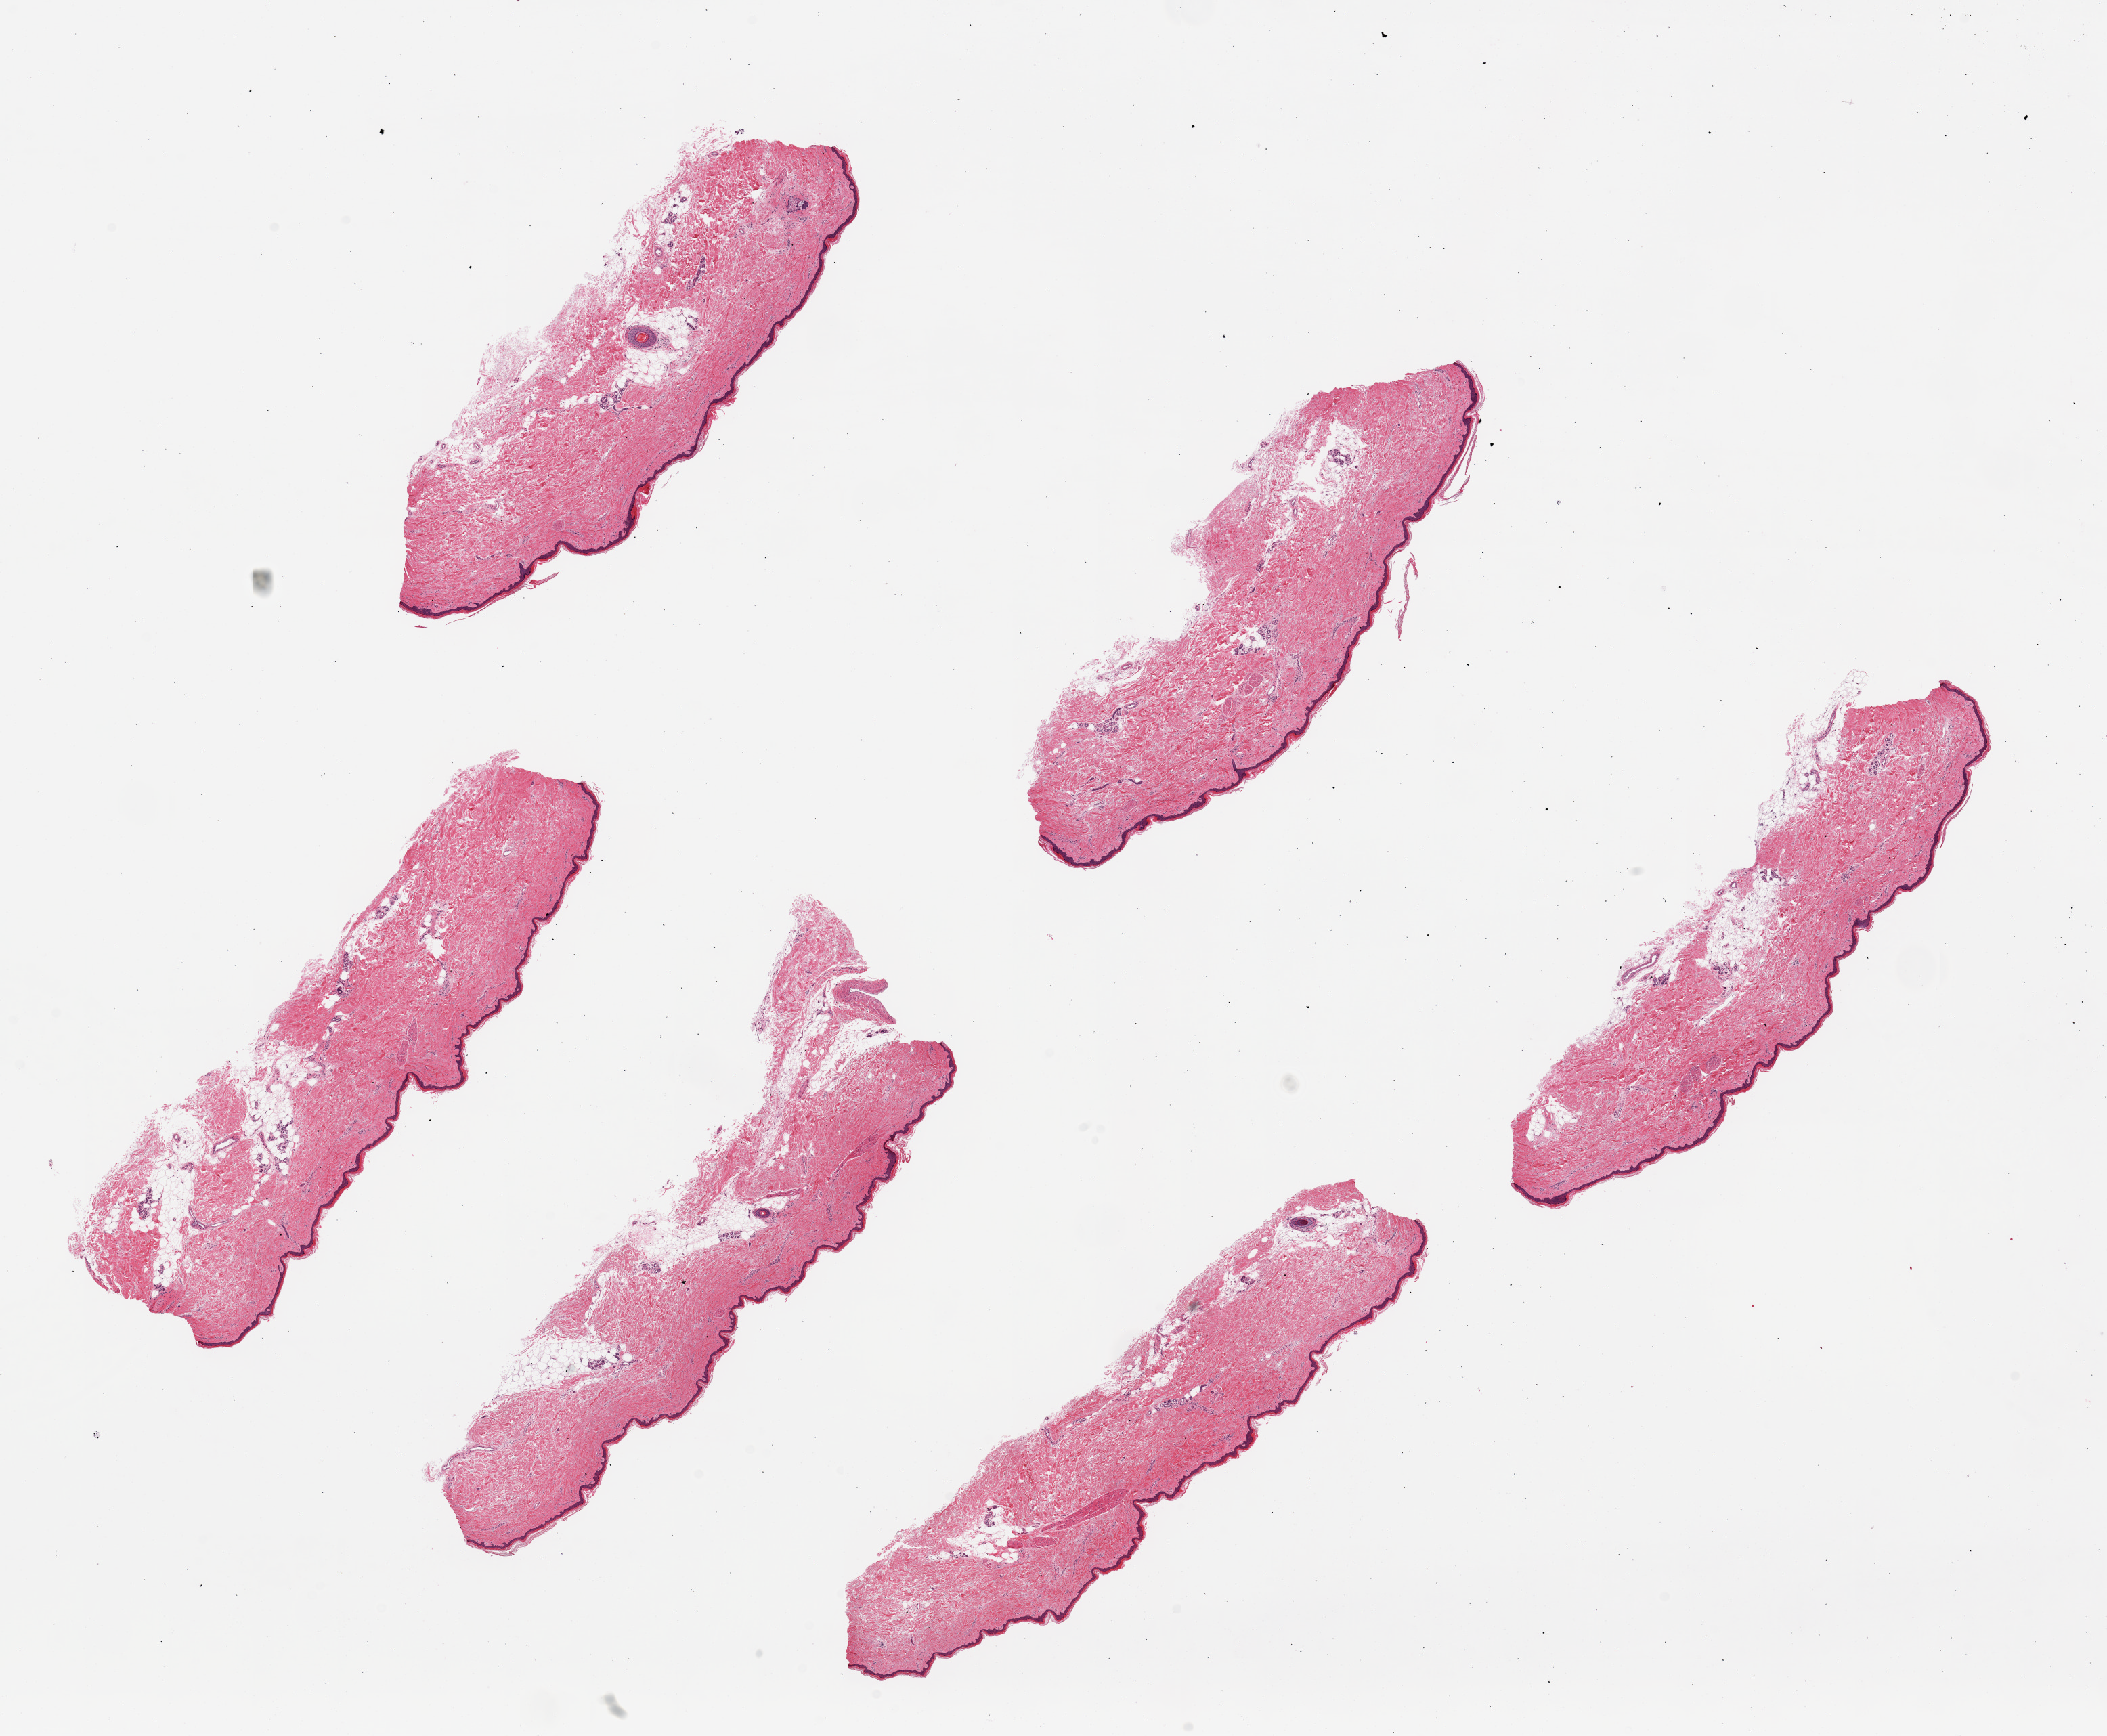
H&E whole-slide image, shown as a low-resolution overview of the whole scanned area (about 24.6 x 20.3 mm, from a 20x scan); PAXgene-fixed, paraffin-embedded tissue; target tissue: skin of lower leg; donor tissue sample. Donor sex: female.
Reviewer comment on this tissue sample: 6 pieces, up to 8x3mm; well trimmed, virtually free of subcutaneous adipose.